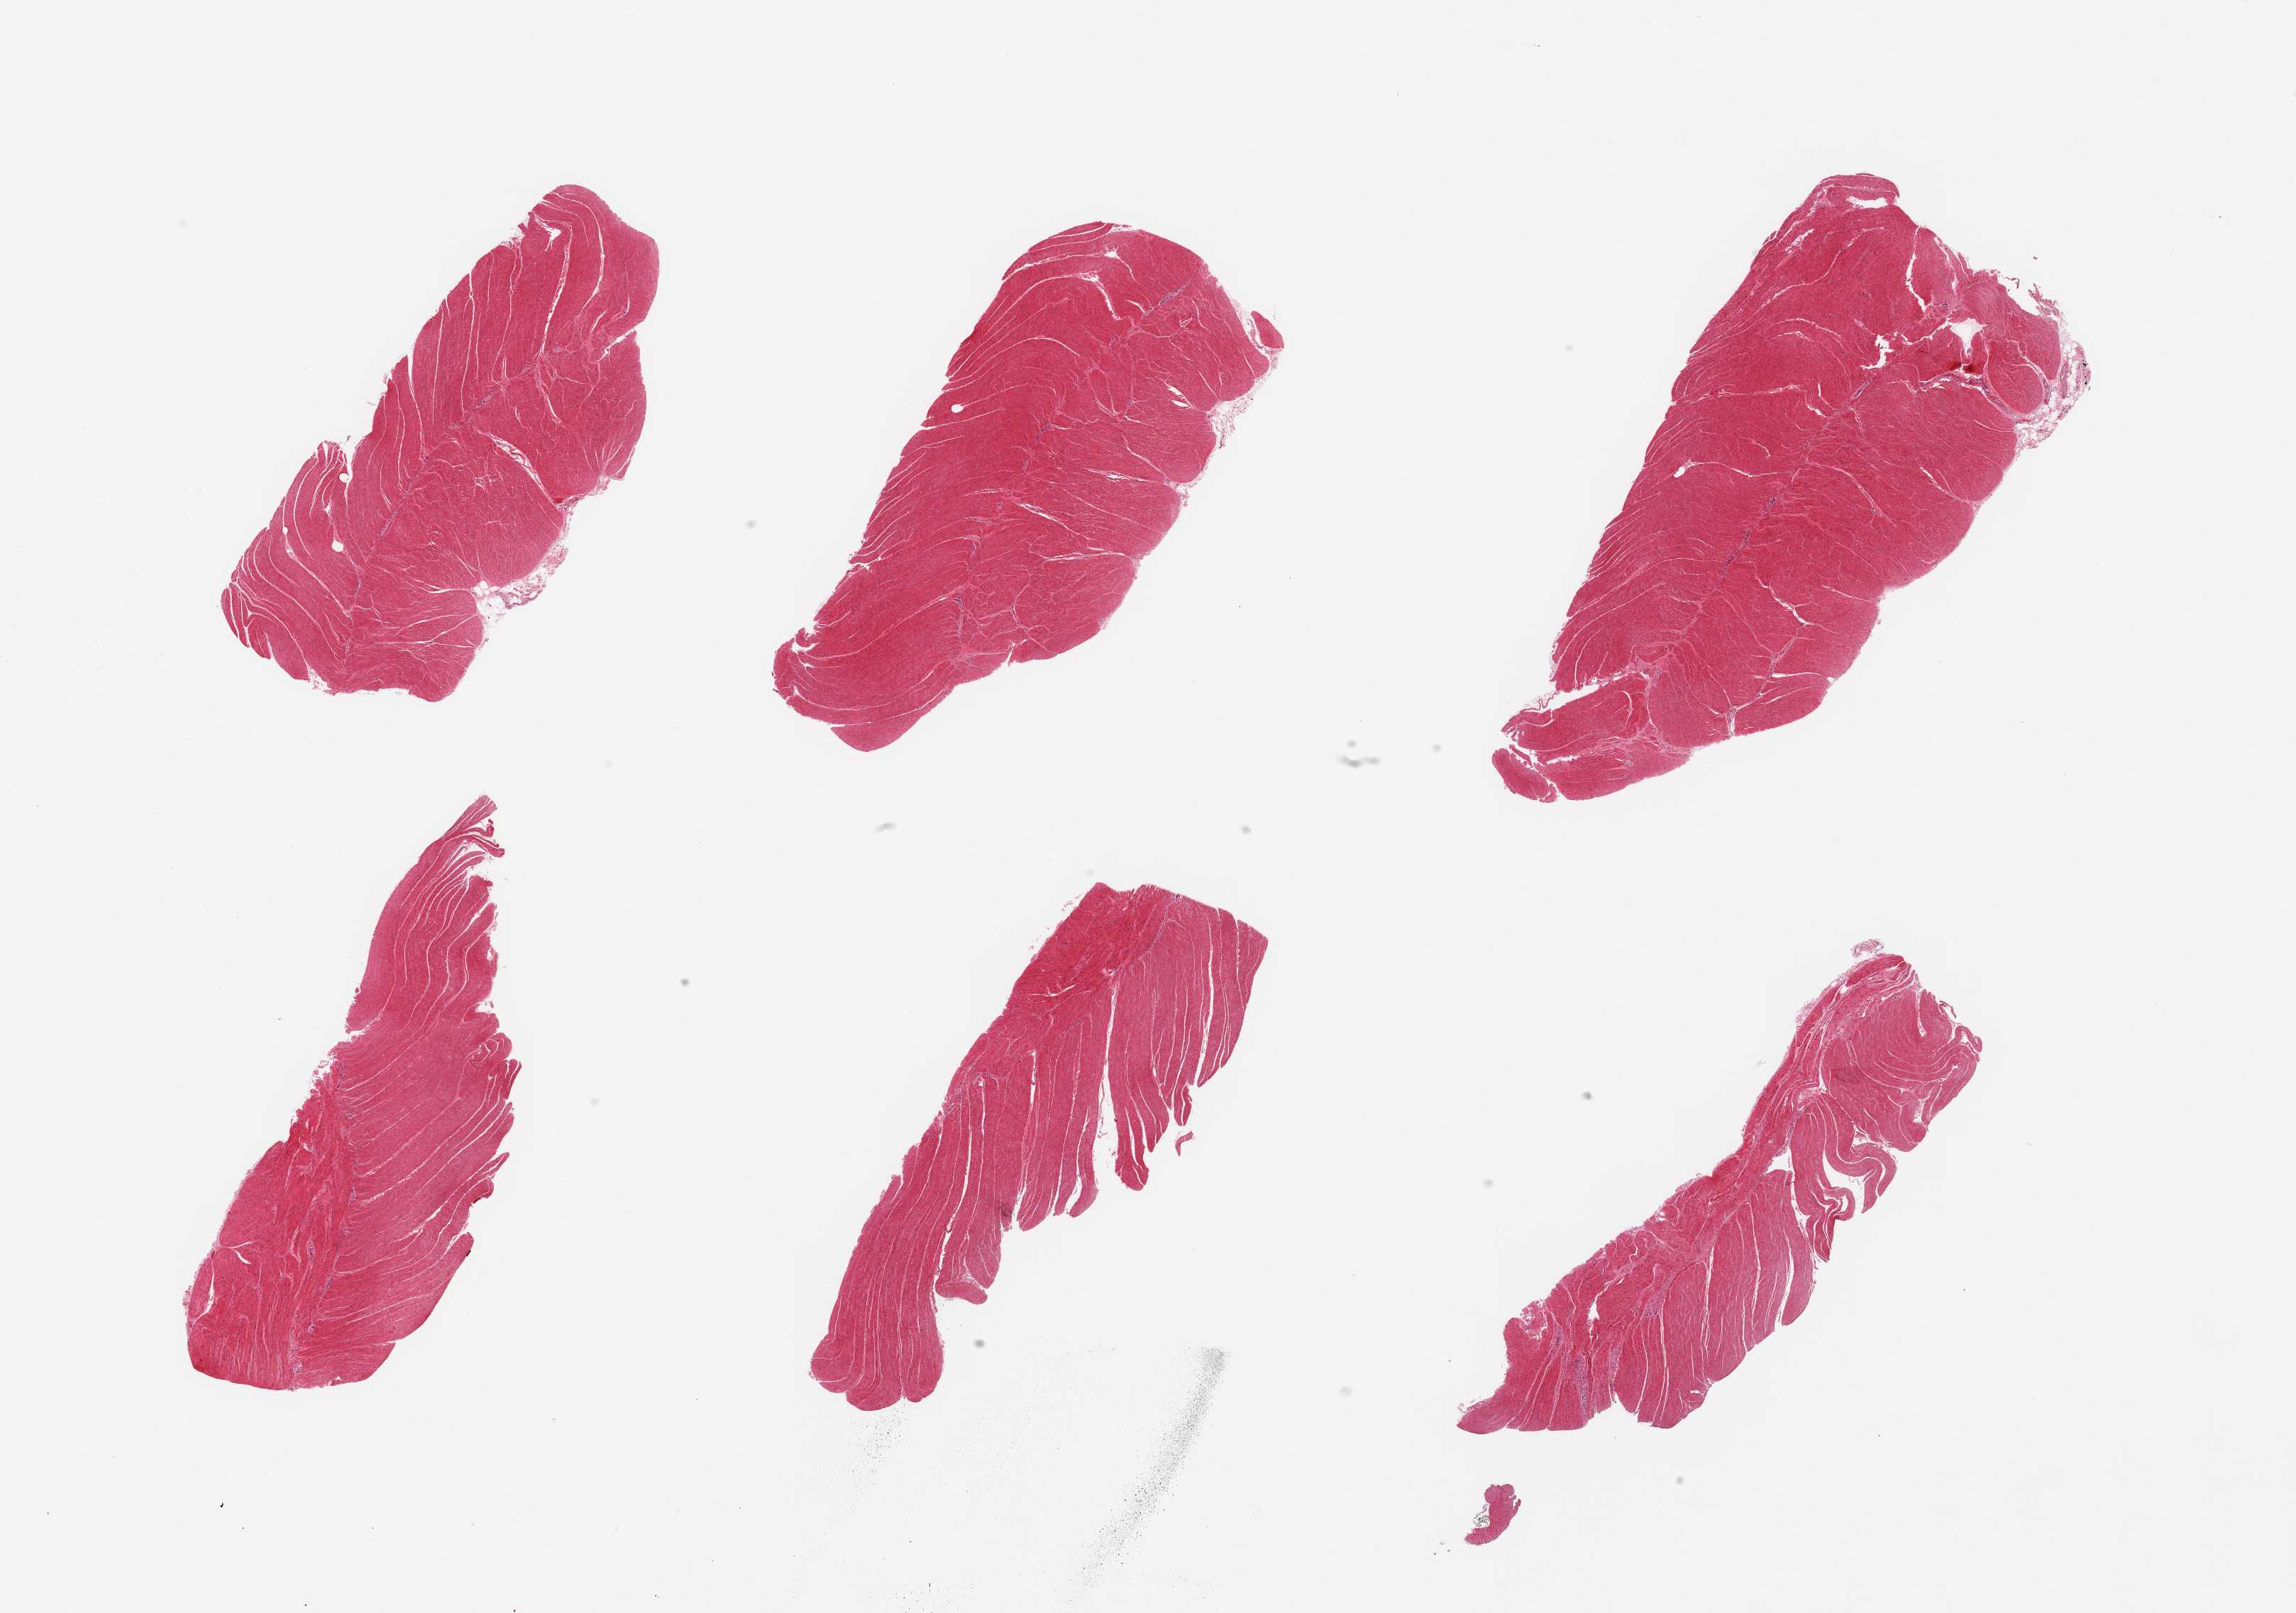
Whole-slide image, hematoxylin and eosin (H&E) stain, whole scanned area (about 25.6 x 18.0 mm, from a 20x scan) shown as a low-resolution overview, PAXgene-fixed paraffin-embedded (PFPE) section, target tissue: sigmoid colon, donor tissue sample. Donor sex: male.
• reviewer comment on this tissue sample: 6 pieces; well trimmed target muscularis